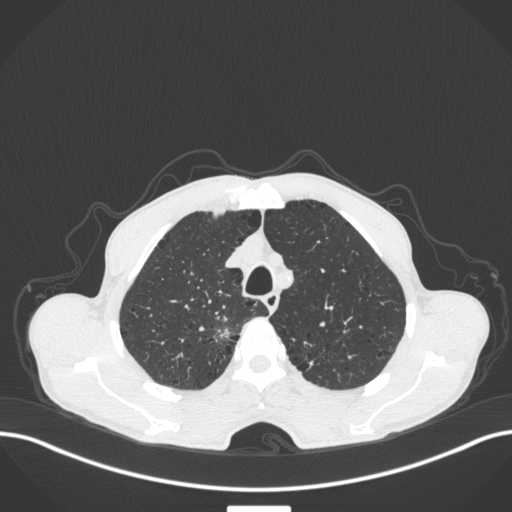
Chest CT, one axial slice. Slice 343 of 445 in the series (ordered by position). Lung window (W 1500 / L -600 HU). 1 mm slice thickness. 512 × 512 image matrix, field of view 400 × 400 mm. Male patient, age 70 years. From the clinical record (not read from this slice): clinical TNM (as recorded): T1a N0 M0; histopathological grade: G1-2.
Annotated regions visible in this slice (bounding box drawn by a radiologist):
- lung tumour (recorded histology: adenocarcinoma): bounding box [x1, y1, x2, y2] px = [210, 321, 233, 349]